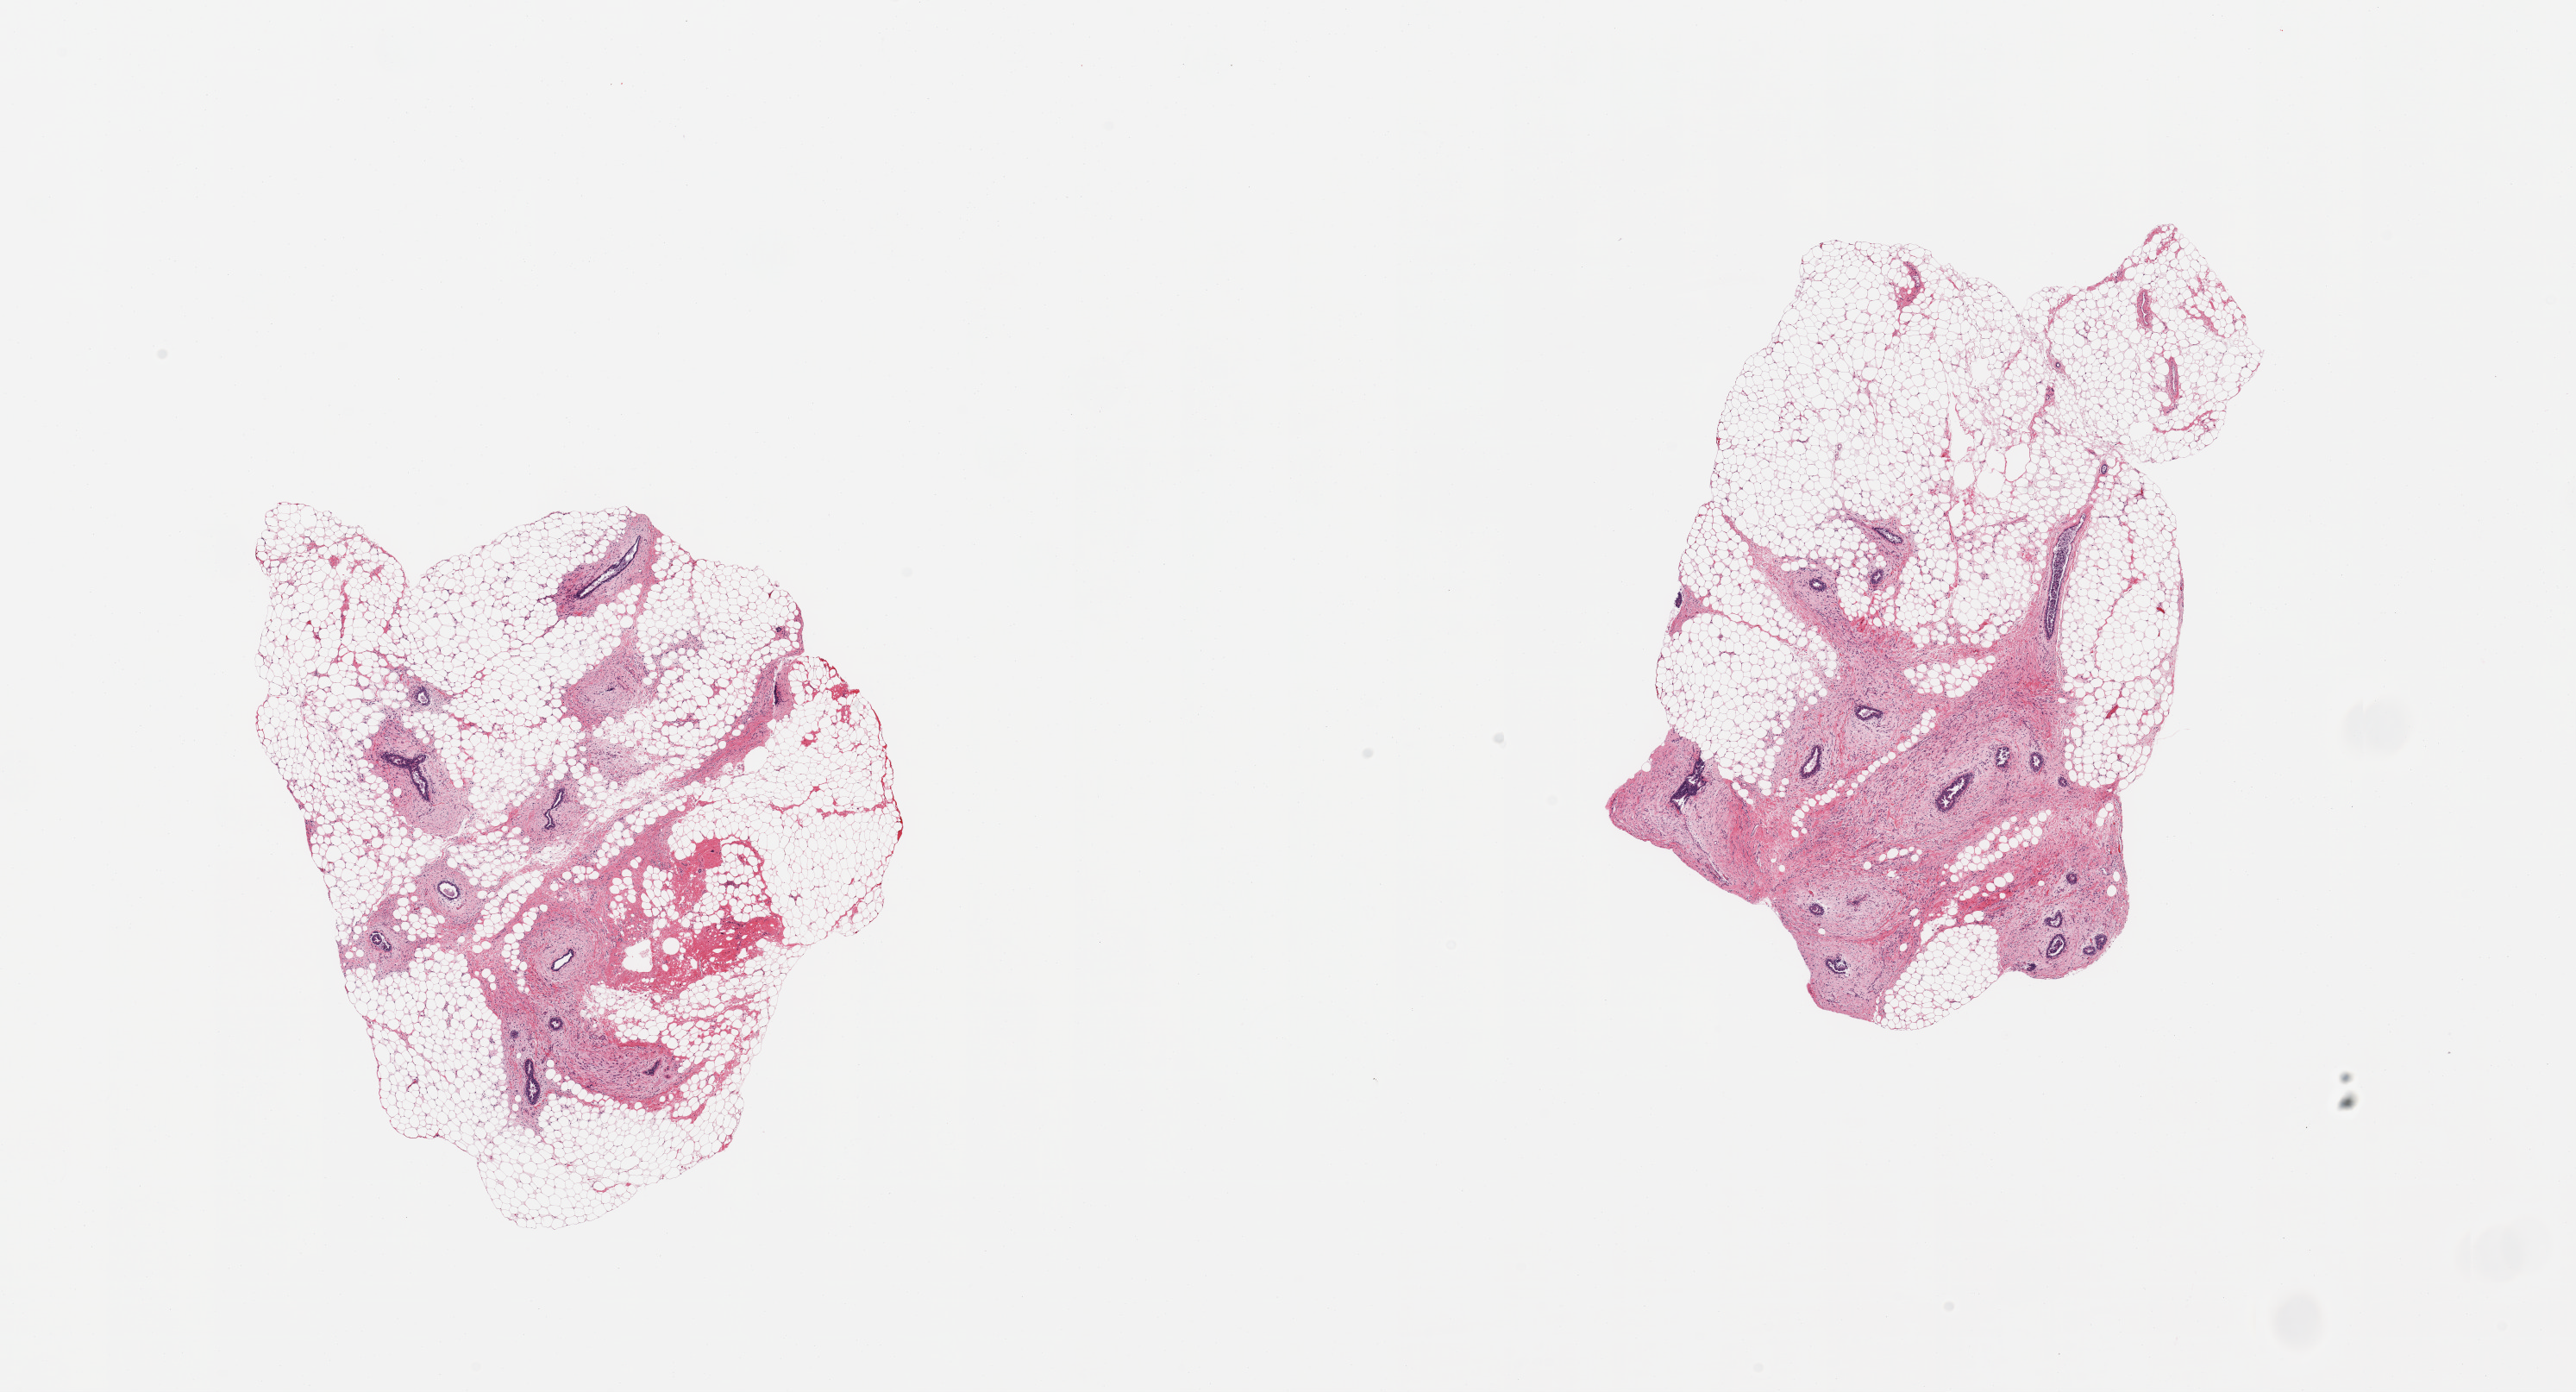
Whole-slide image, haematoxylin and eosin stain, shown as a low-resolution overview of the whole scanned area (about 23.6 x 12.8 mm, from a 20x scan), PAXgene-fixed, paraffin-embedded tissue, sampled site (target tissue): breast, tissue donor sample. Donor: male.
Reviewer comment on this tissue sample: 2 pieces; adipose tissue and ductal structures embedded in loose, cellular connective tissue, c/w gynecomastoid change.